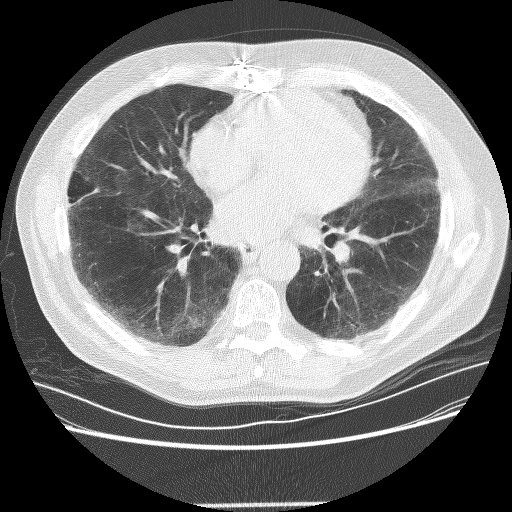
Axial slice from a low-dose chest CT screening exam, baseline annual screen, lung window (W 1500 / L -600 HU), 2.5 mm slice thickness, lung (sharp) reconstruction kernel (BONE), 120 kVp, slice 145 of 281 in the series. Male, age 72 years at enrolment. Former smoker at enrolment.
- Lesion marked by an expert reader, bounding box (x1, y1, x2, y2) in pixels: (171, 306, 211, 343).
- The screening reader recorded 2 non-calcified nodules or masses ≥4 mm on this exam (right lower lobe, left lower lobe); which of them this box marks is not recorded.
- Official screen result: positive, change unspecified: nodule(s) >= 4 mm or enlarging nodule(s), mass(es), or other non-specific abnormalities suspicious for lung cancer.